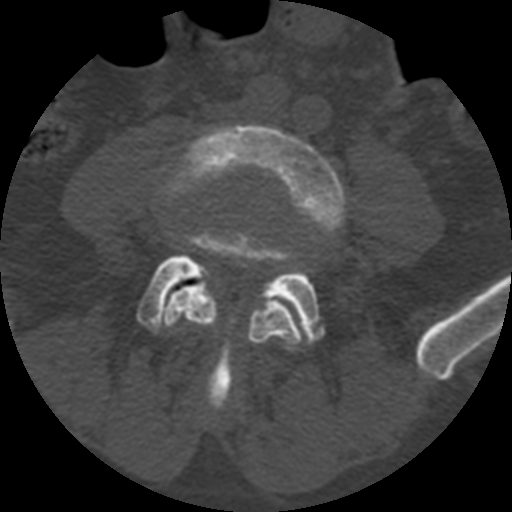
CT including the spine, one axial slice. Position 268 of 399 along the scan axis. Bone window (W 1800 / L 400 HU). 512 × 512 image matrix, field of view 160 × 160 mm. Patient age 71 years. From the clinical record (not read from this slice): primary cancer: prostate.
Annotated regions visible in this slice (semi-automatic segmentation, software-assisted and operator-edited):
- L4 vertebra: bounding box [x1, y1, x2, y2] px = [161, 124, 345, 400]
- L5 vertebra: [136, 233, 326, 411]